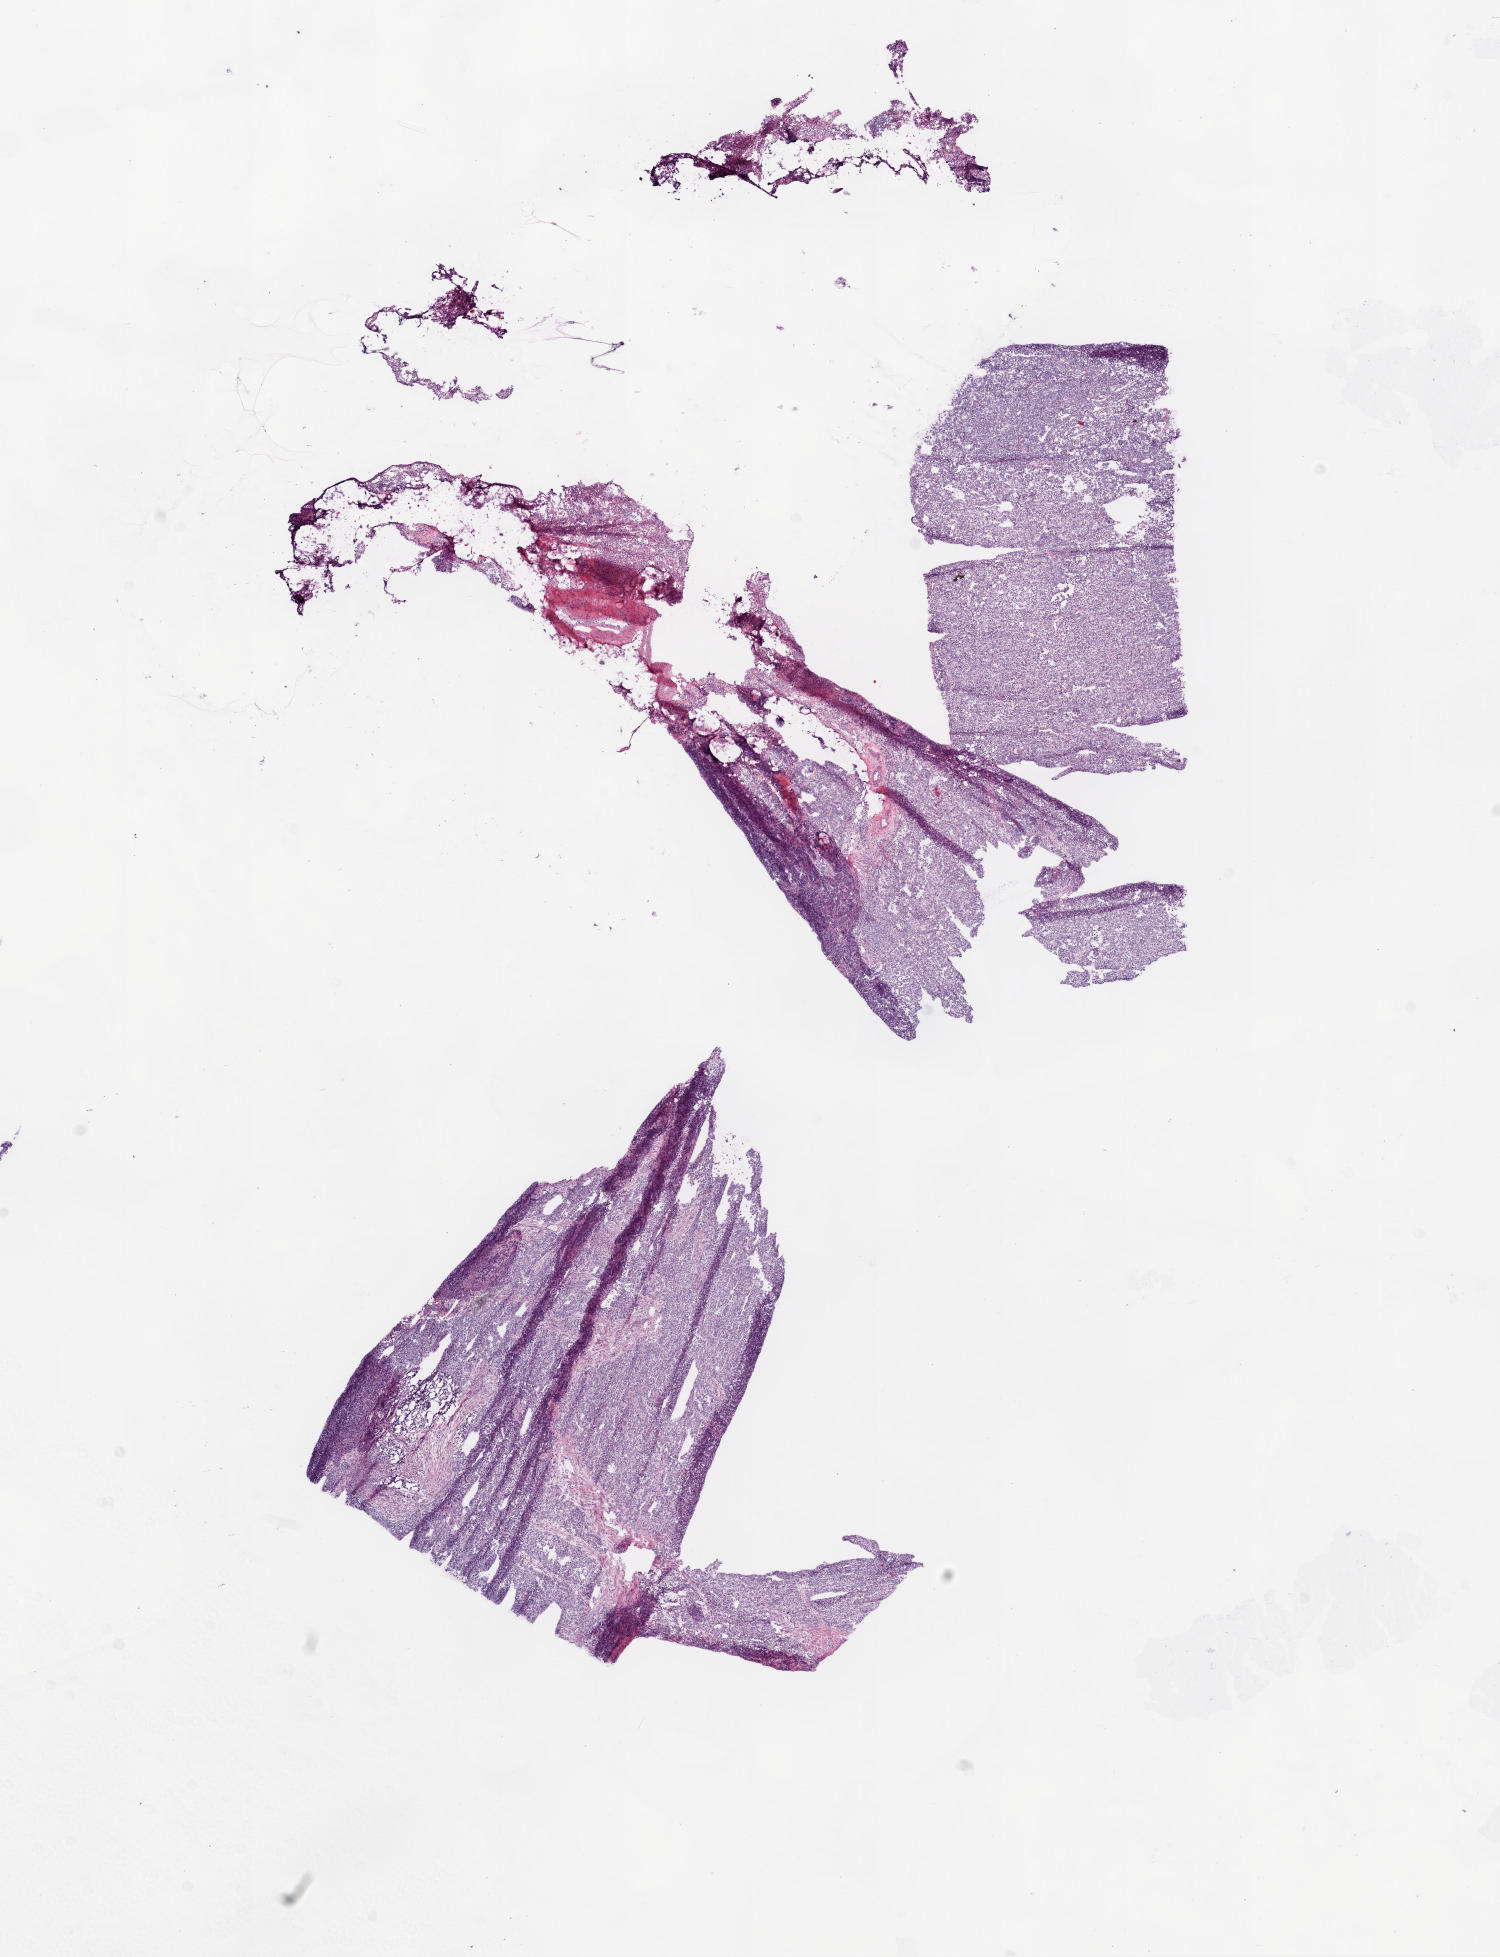
Digitized H&E-stained tissue section (whole slide), shown as a low-resolution overview of the whole scanned area (about 12.0 x 15.7 mm, acquisition: 20x scan); frozen section from the bottom of the tissue portion; primary tumour sample from the ovary. Female patient; age at initial diagnosis 58 years. Histologic grade: G3 (poorly differentiated). Composition of this section per pathologist review: tumour cells 90%, tumour nuclei 90%, normal cells 0%, stromal cells 10%, necrosis 0%. Inflammatory infiltration, as recorded: lymphocyte infiltration 0%, monocyte infiltration 0%, neutrophil infiltration 0%.
• FIGO stage: IIIC
• histologic diagnosis: Serous cystadenocarcinoma, NOS